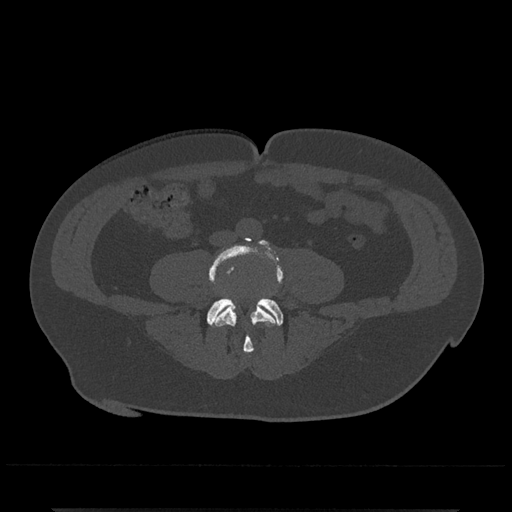
CT including the spine, one axial slice; slice 124 of 797 in the series (ordered by position); bone window (W 1800 / L 400 HU); 0.5 mm slice thickness; 512 × 512 image matrix, field of view 393 × 393 mm. Male patient, age 67 years. Case-level facts recorded for this patient, not image findings: primary cancer: prostate.
Outlined on this slice (semi-automatically segmented with operator editing):
- L4 vertebra: bounding box (x1, y1, x2, y2) in pixels: (209, 240, 283, 354)
- L5 vertebra: (207, 297, 283, 325)